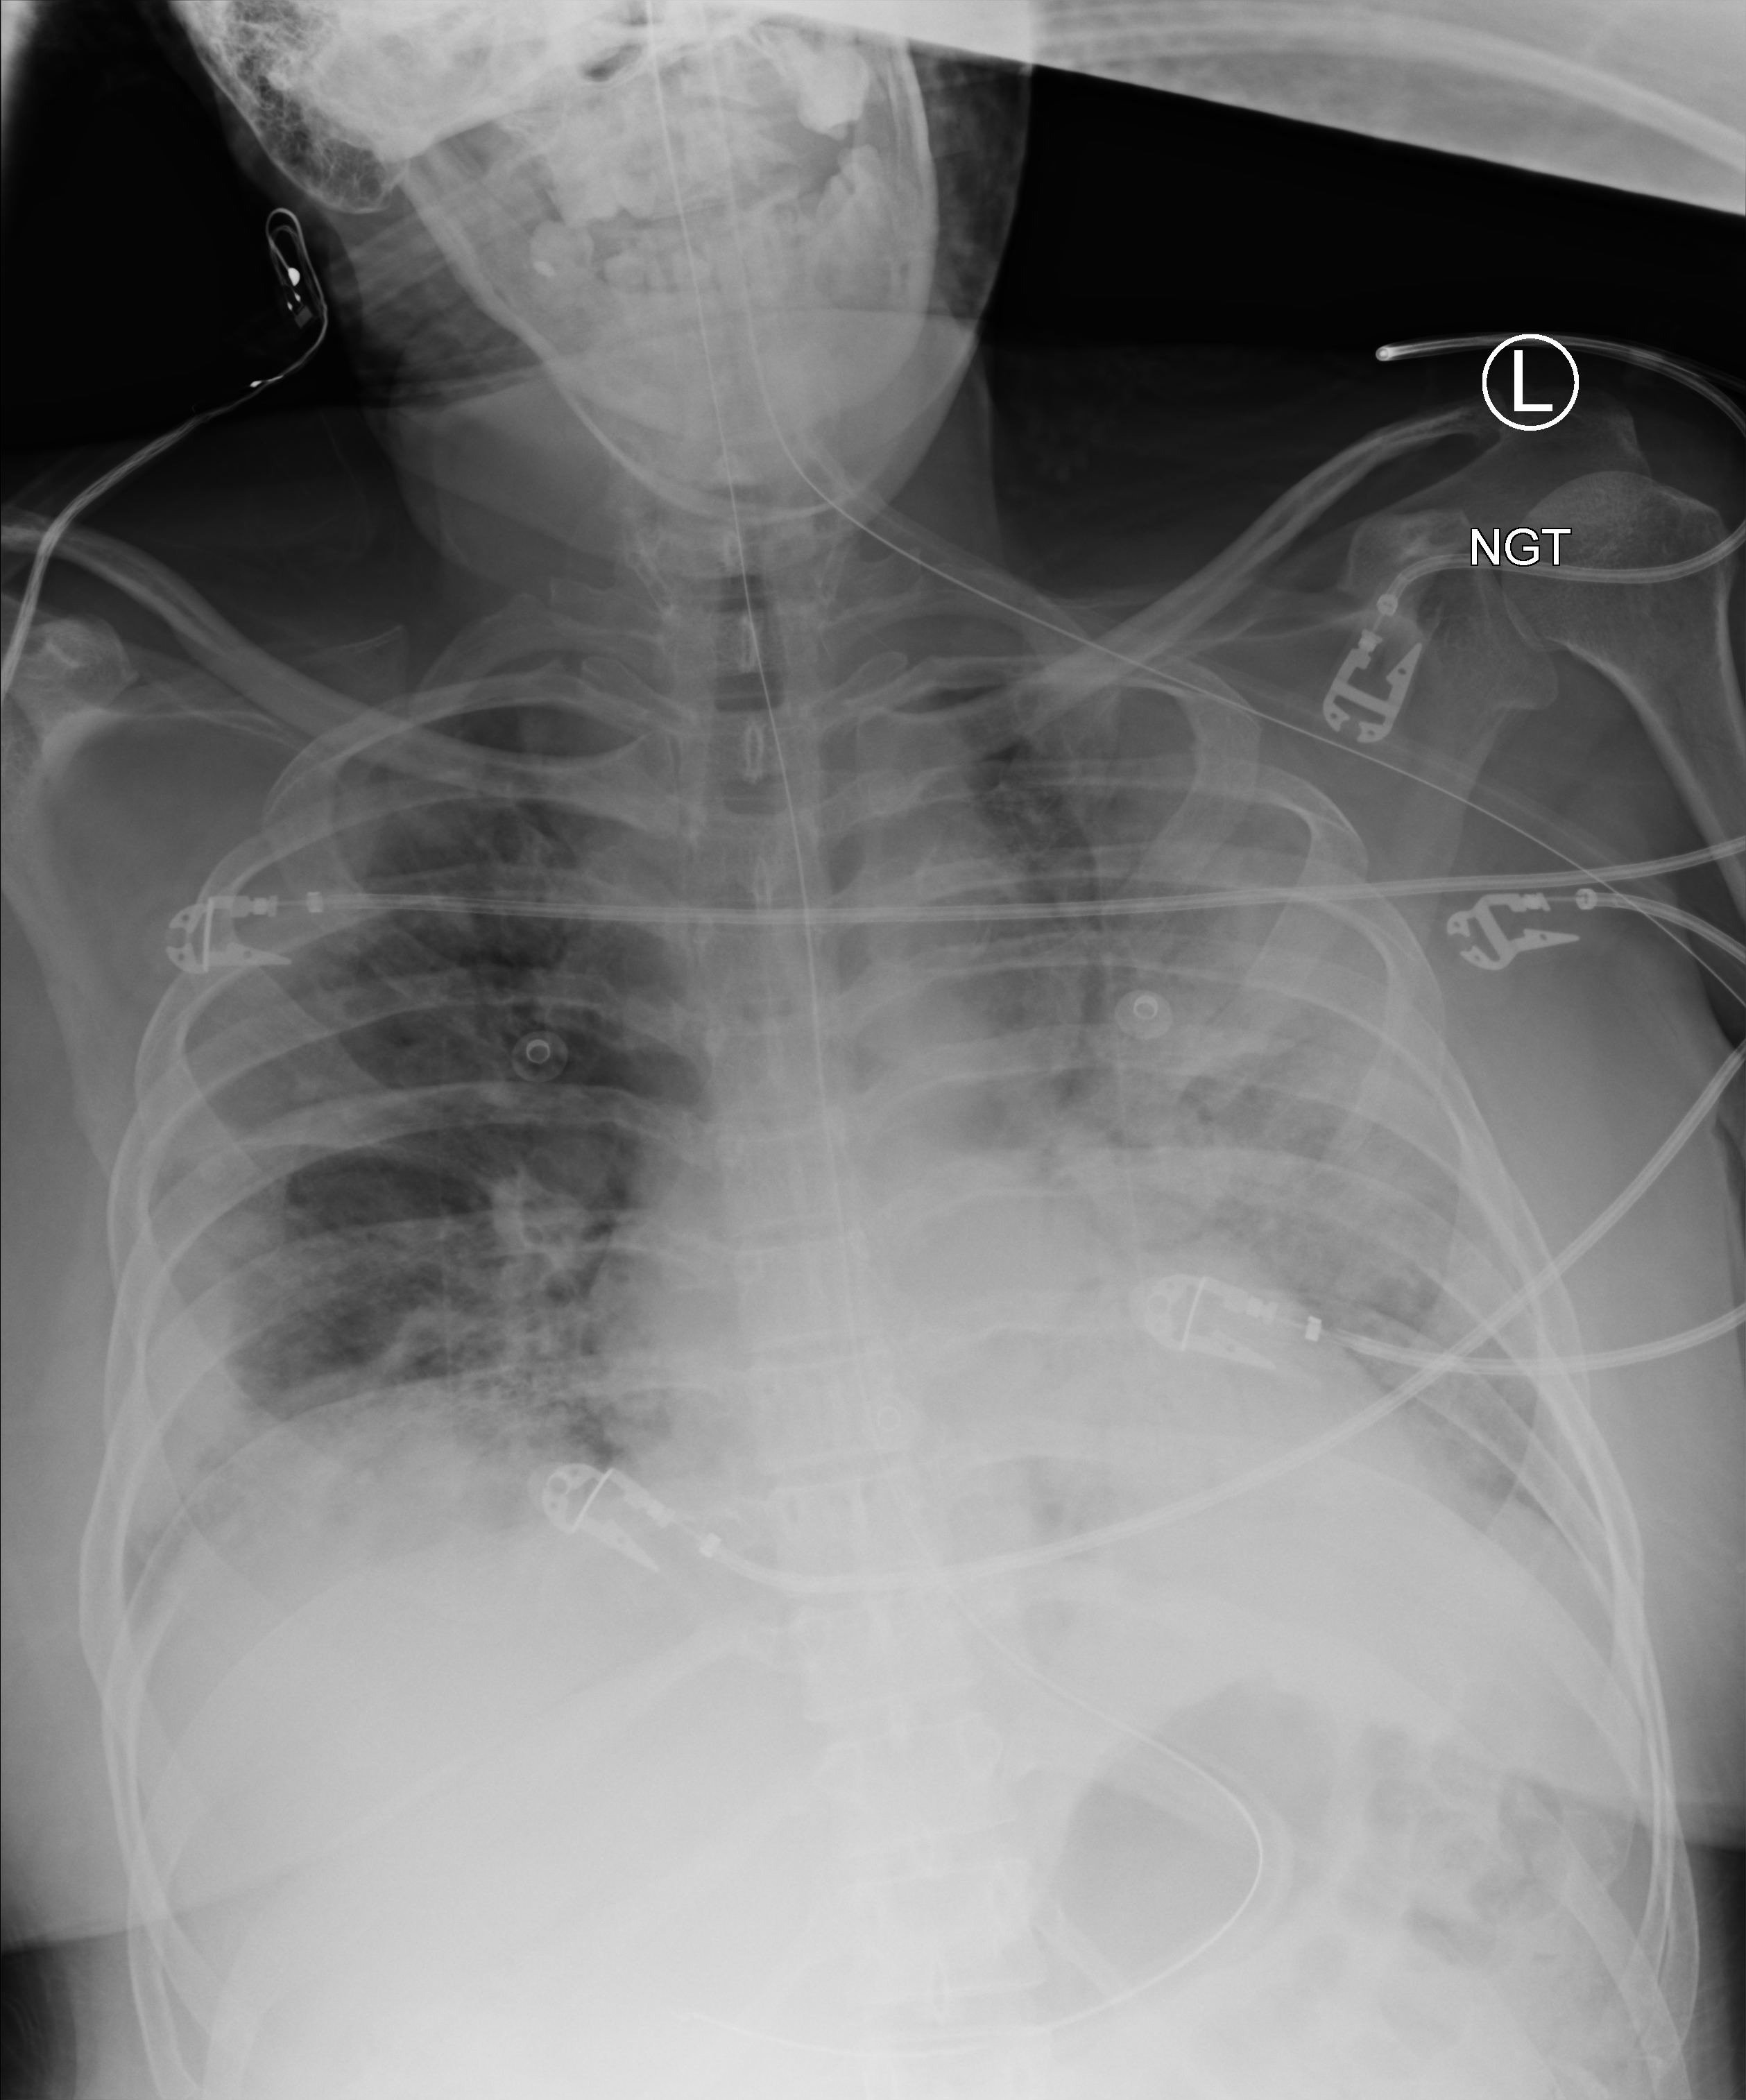
Bedside chest radiograph (computed radiography), anteroposterior (AP) projection. Patient hospitalised with COVID-19, aged 18–59 years.
Admission-level facts for this patient (not findings on this image; timing relative to this image not recorded): smoking status (admission record): never; mechanically ventilated during this hospital stay: yes; admitted to intensive care during this hospital stay: yes.